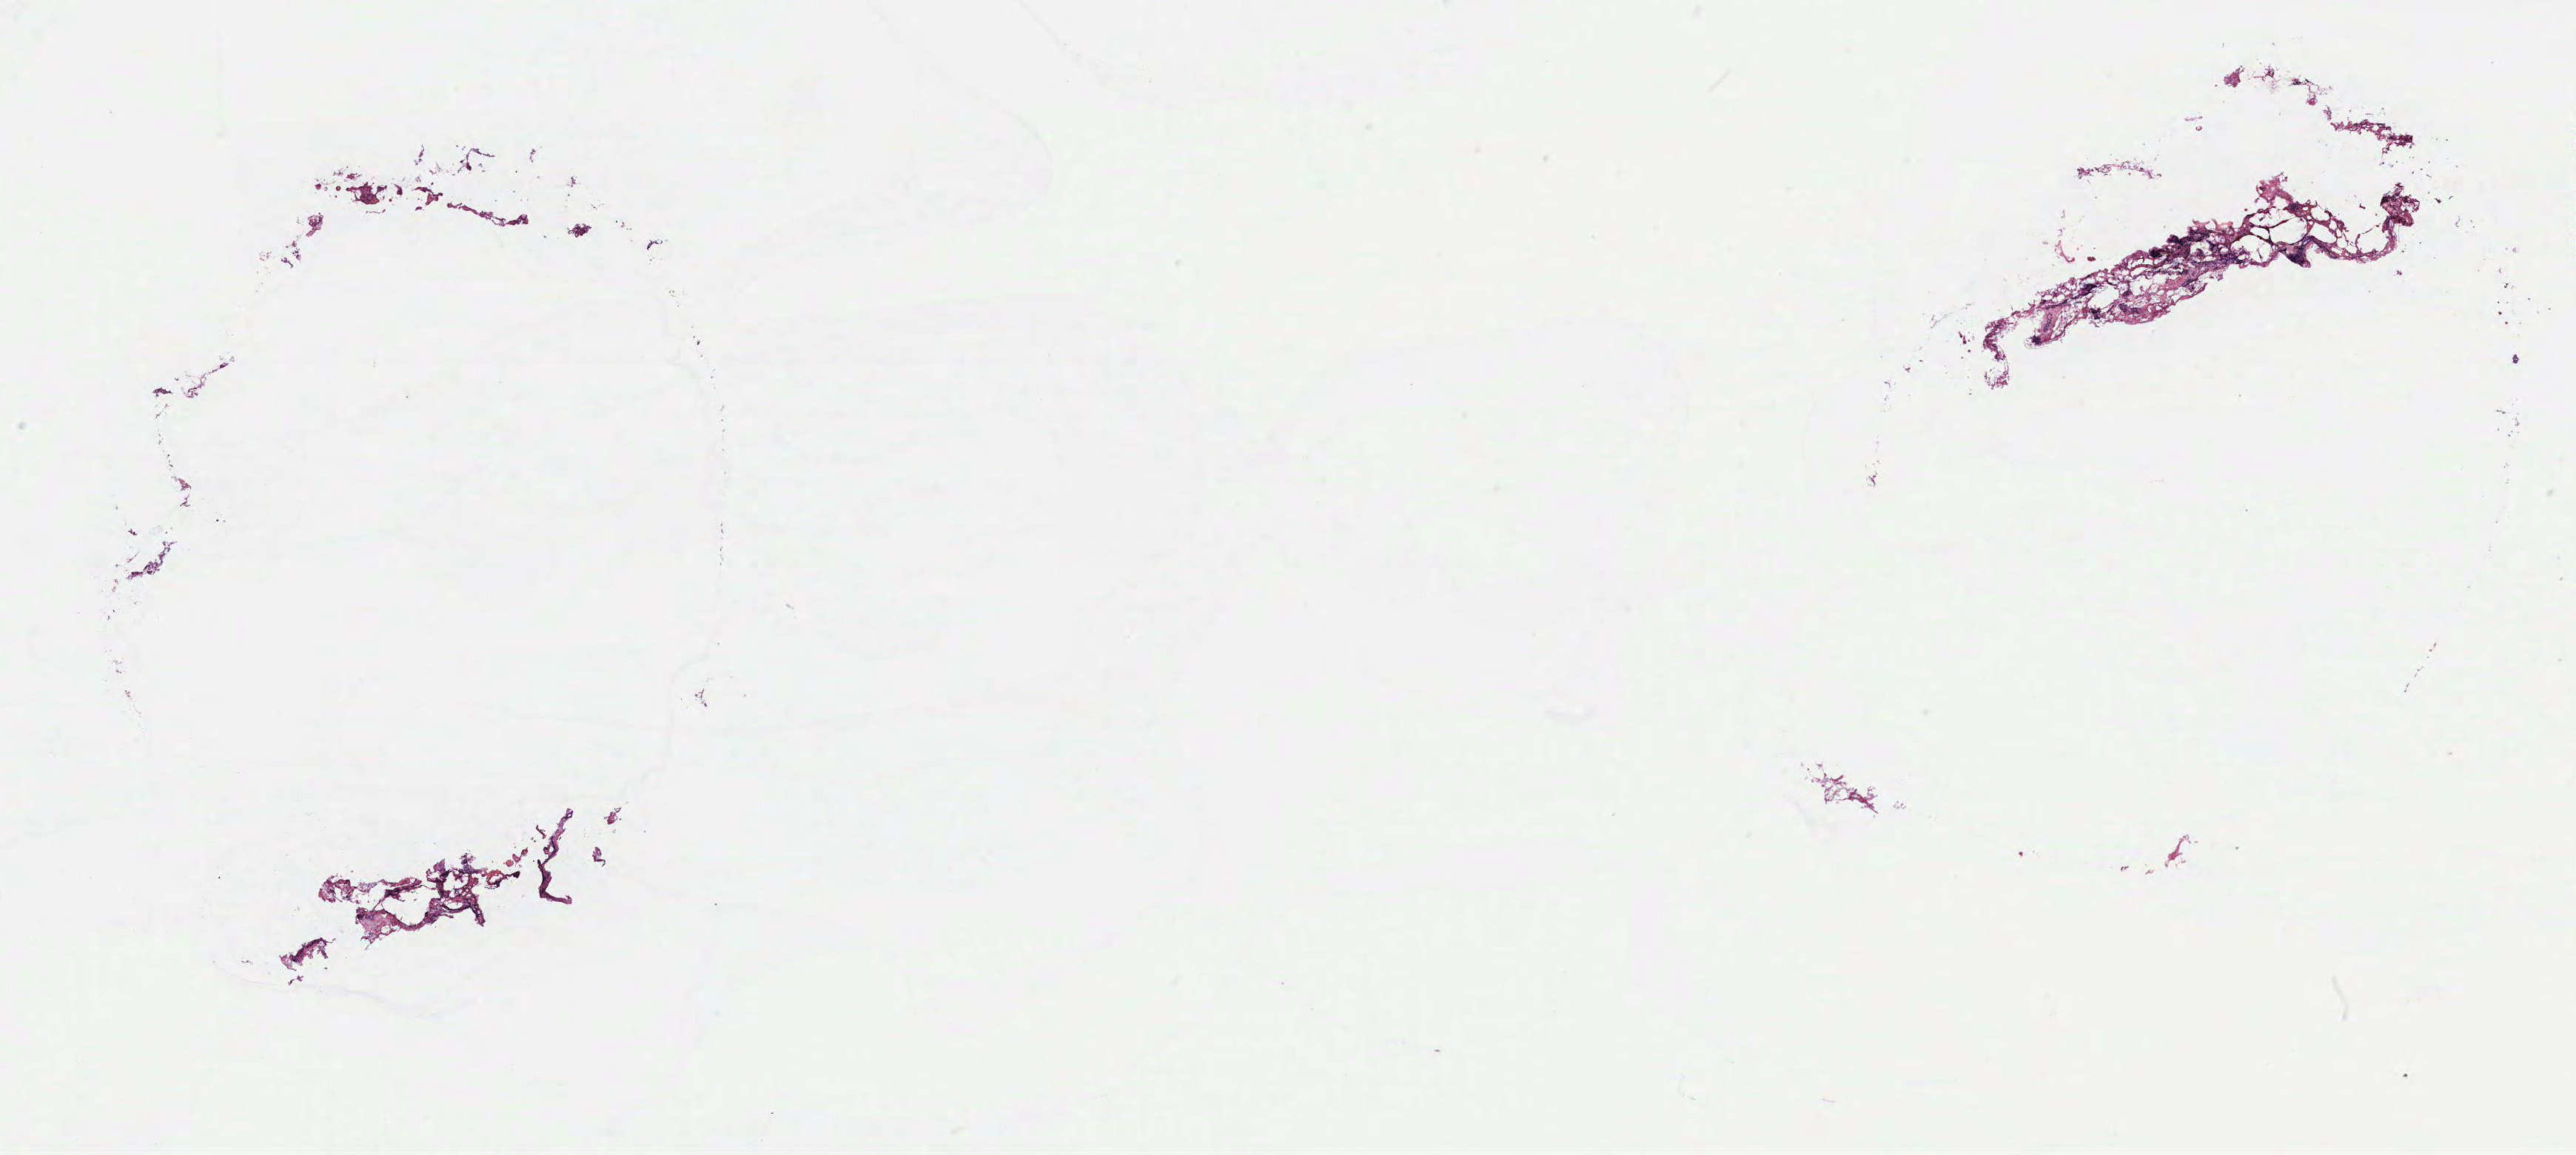
Whole-slide histology image, H&E-stained, a low-resolution overview of the entire scanned area, about 27.9 x 12.5 mm (slide scanned at 40x). Breast, tissue type not recorded.
* patient diagnosis (cohort enrolment): breast cancer (breast)